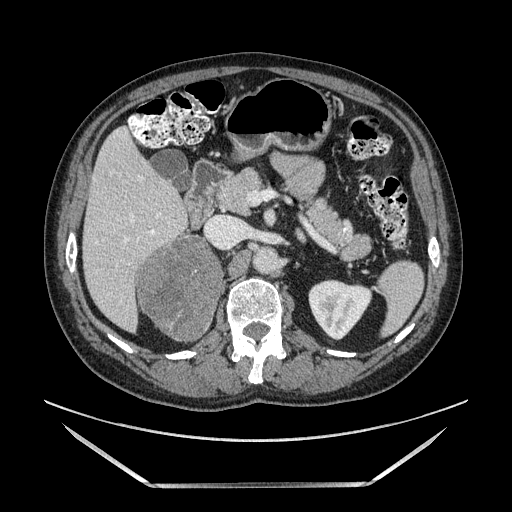
Contrast-enhanced abdominal CT, one axial slice. Slice 73 of 185 in the series (ordered by position). Soft-tissue window (W 400 / L 40 HU). 1.25 mm slice thickness. 512 × 512 image matrix, field of view 440 × 440 mm. Male patient. Case-level facts recorded for this patient, not image findings: diagnosis: adrenocortical carcinoma; tumour side: right adrenal; tumour size at pathology: 10.3 cm; Ki-67 index: 20 %; stage (as recorded): 3.
Annotated regions visible in this slice (semi-automatic segmentation, software-assisted and operator-edited):
- mass: bounding box [x1, y1, x2, y2] px = [141, 238, 222, 339]